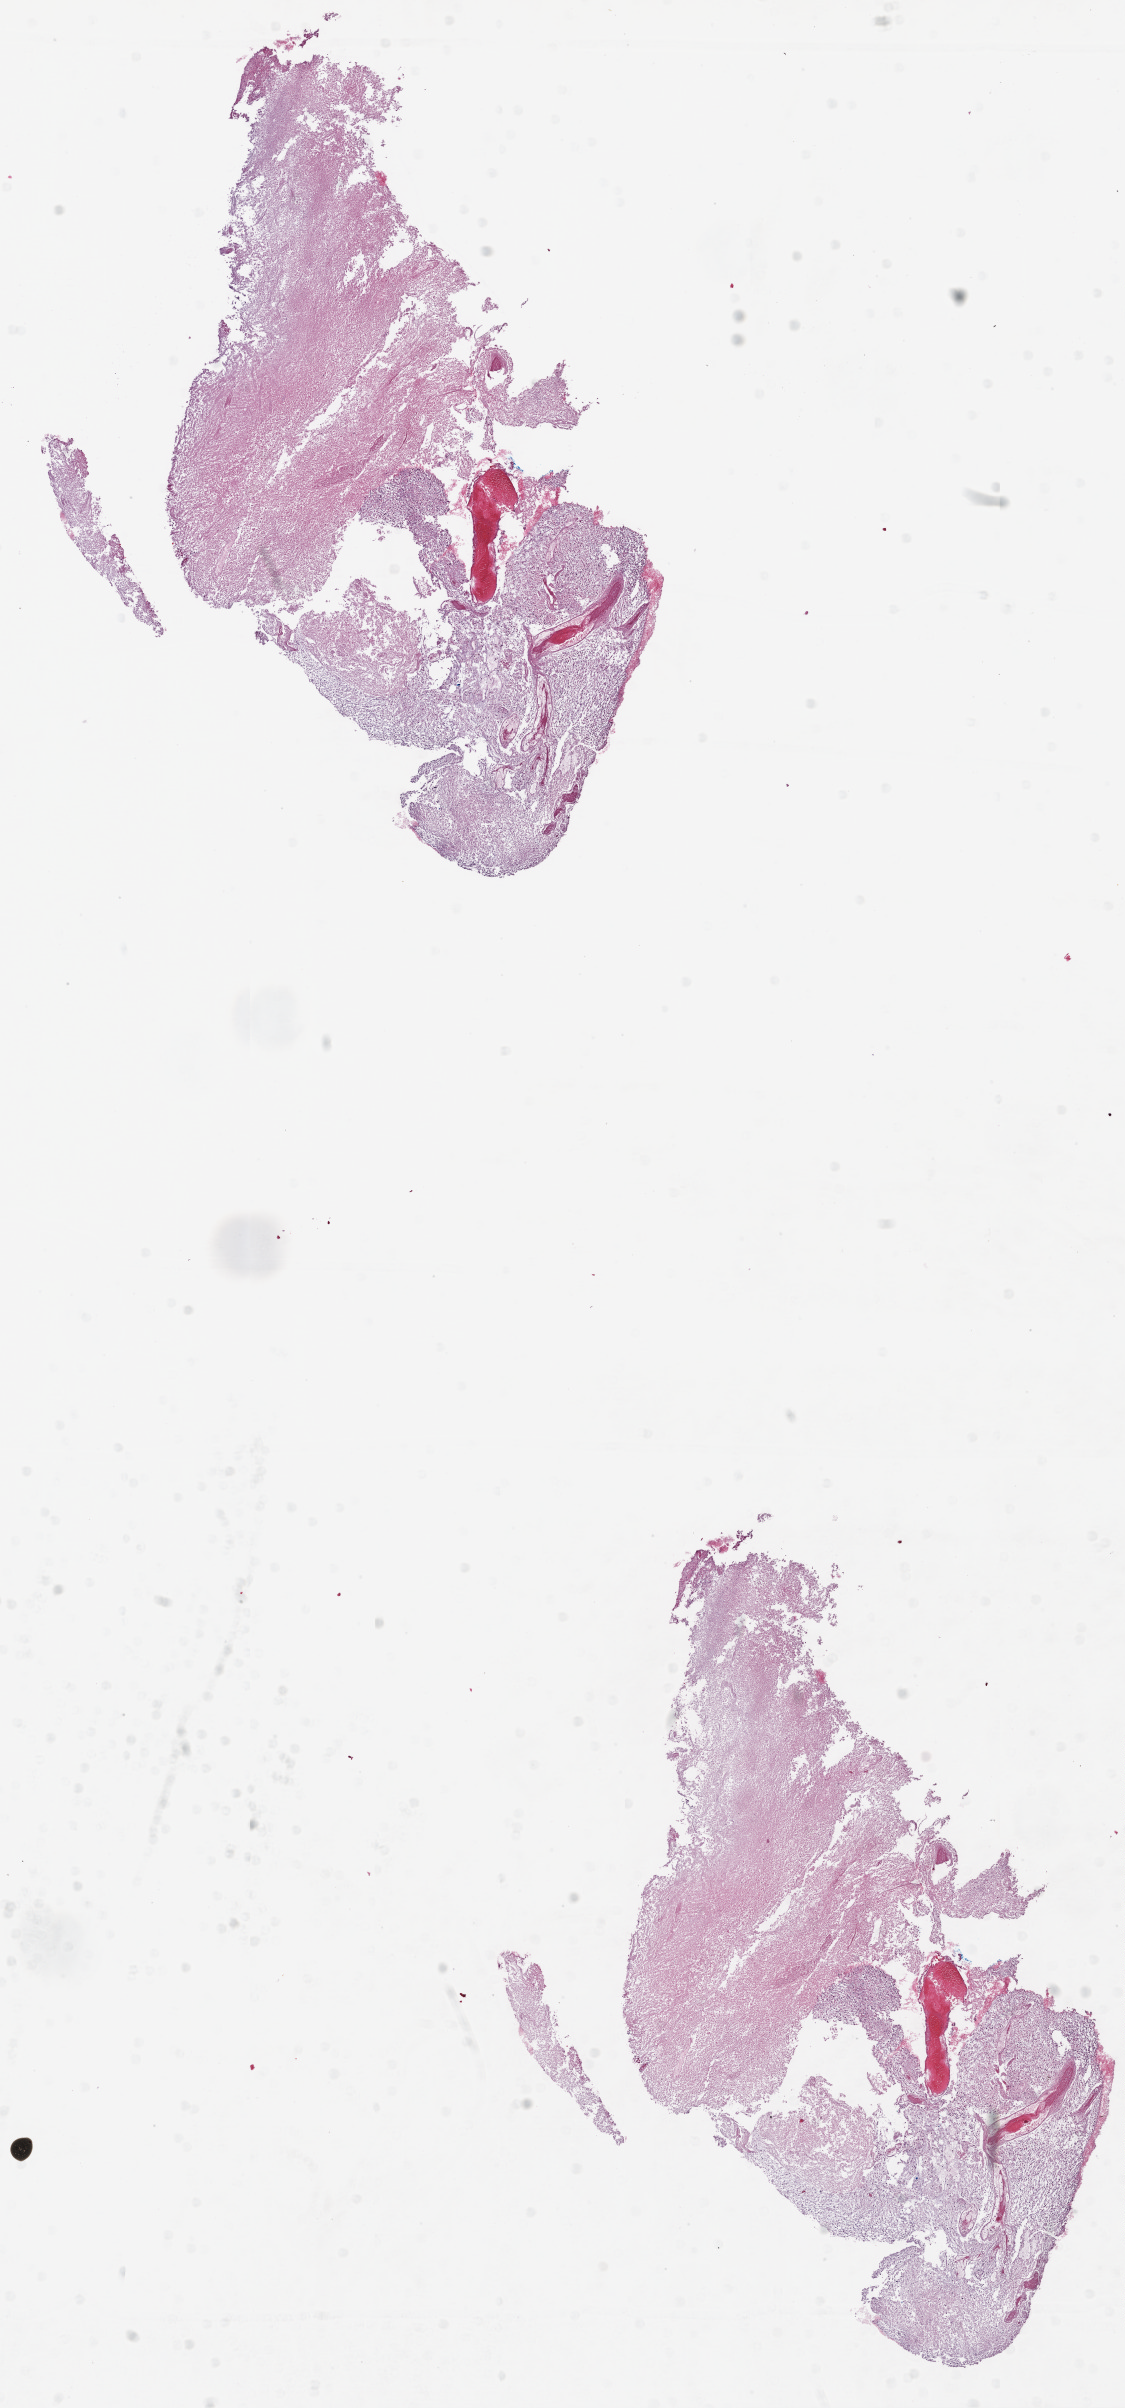
Whole-slide histology image, H&E-stained — shown as a low-resolution overview of the whole scanned area (about 9.0 x 19.3 mm, from a 20x scan). FFPE section. Brain, primary tumour sample. Male, age 59 years at initial diagnosis.
Histologic diagnosis: Glioblastoma.